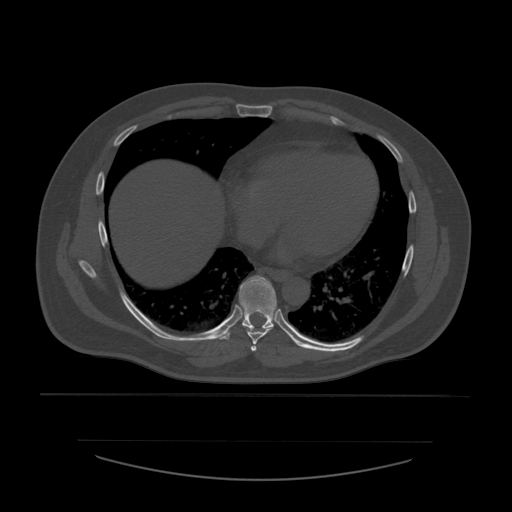
CT including the spine, one axial slice; position 348 of 532 along the scan axis; 120 kVp; bone window (W 1800 / L 400 HU); 512 × 512 image matrix, field of view 441 × 441 mm. Patient age 44 years. Case-level facts recorded for this patient, not image findings: primary cancer: soft tissue sarcoma.
Annotated regions visible in this slice (semi-automatically segmented with operator editing):
- T6 vertebra: box from (x=251, y=346) to (x=257, y=353) px
- T7 vertebra: (x=242, y=325)–(x=273, y=345)
- T8 vertebra: (x=219, y=276)–(x=277, y=340)